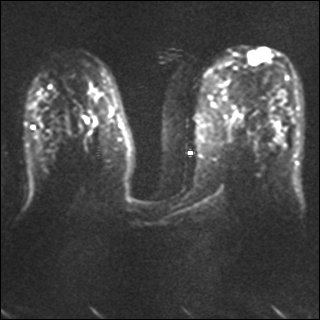
Breast MRI, one axial slice. Position 20 of 40 along the scan axis. Diffusion-weighted series; image 2 of 4 stored at this slice position (different b-values; order by instance number). 1.5 T. 4 mm slice thickness. 320 × 320 image matrix. Female patient.
Outlined on this slice (outlined manually by an expert reader):
- tumour on diffusion-weighted imaging: bounding box (x1, y1, x2, y2) in pixels: (248, 51, 266, 64)